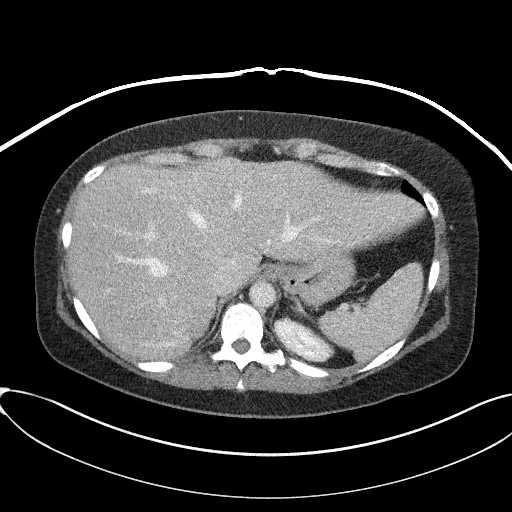
Contrast-enhanced abdominal CT, one axial slice. Position 67 of 95 along the scan axis. 100 kVp. Soft-tissue window (W 400 / L 40 HU). 3 mm slice thickness. 512 × 512 image matrix. Female patient, age 46 years. Case-level facts recorded for this patient, not image findings: diagnosis: adrenocortical carcinoma; tumour side: right adrenal; tumour size at pathology: 7.2 cm; Ki-67 index: 50 %; stage (as recorded): 4.
Outlined on this slice (semi-automatically segmented with operator editing):
- mass: bounding box [x1, y1, x2, y2] px = [189, 310, 208, 337]